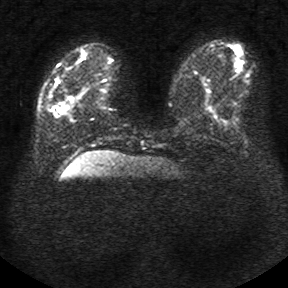
Breast MRI, one axial slice. Position 8 of 34 along the scan axis. Diffusion-weighted series; image 2 of 4 stored at this slice position (different b-values; order by instance number). 1.5 T. 288 × 288 image matrix, field of view 340 × 340 mm. Female patient.
Annotated regions visible in this slice (manually delineated by an expert):
- tumour on diffusion-weighted imaging: bounding box (x1, y1, x2, y2) in pixels: (76, 51, 87, 64)